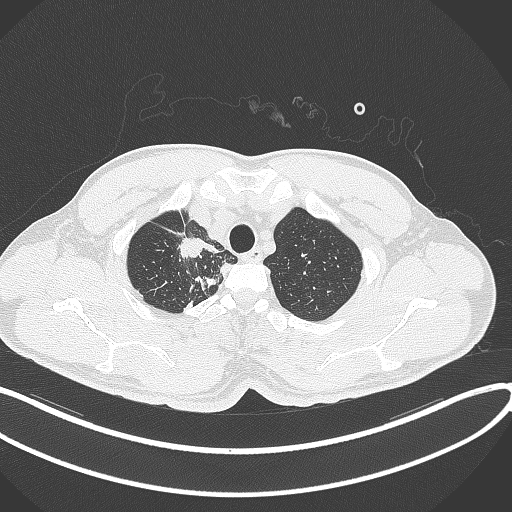
Chest CT, one axial slice; slice 330 of 391 in the series (ordered by position); reconstruction kernel B70f; 120 kVp; lung window (W 1500 / L -600 HU); 1 mm slice thickness; 512 × 512 image matrix. Patient: male, 48 years. From the clinical record (not read from this slice): clinical TNM (as recorded): T1c N1 M1.
Structures marked on this image (rectangle marked by the reading radiologist):
- lung tumour (recorded histology: adenocarcinoma): box from (x=175, y=232) to (x=209, y=264) px